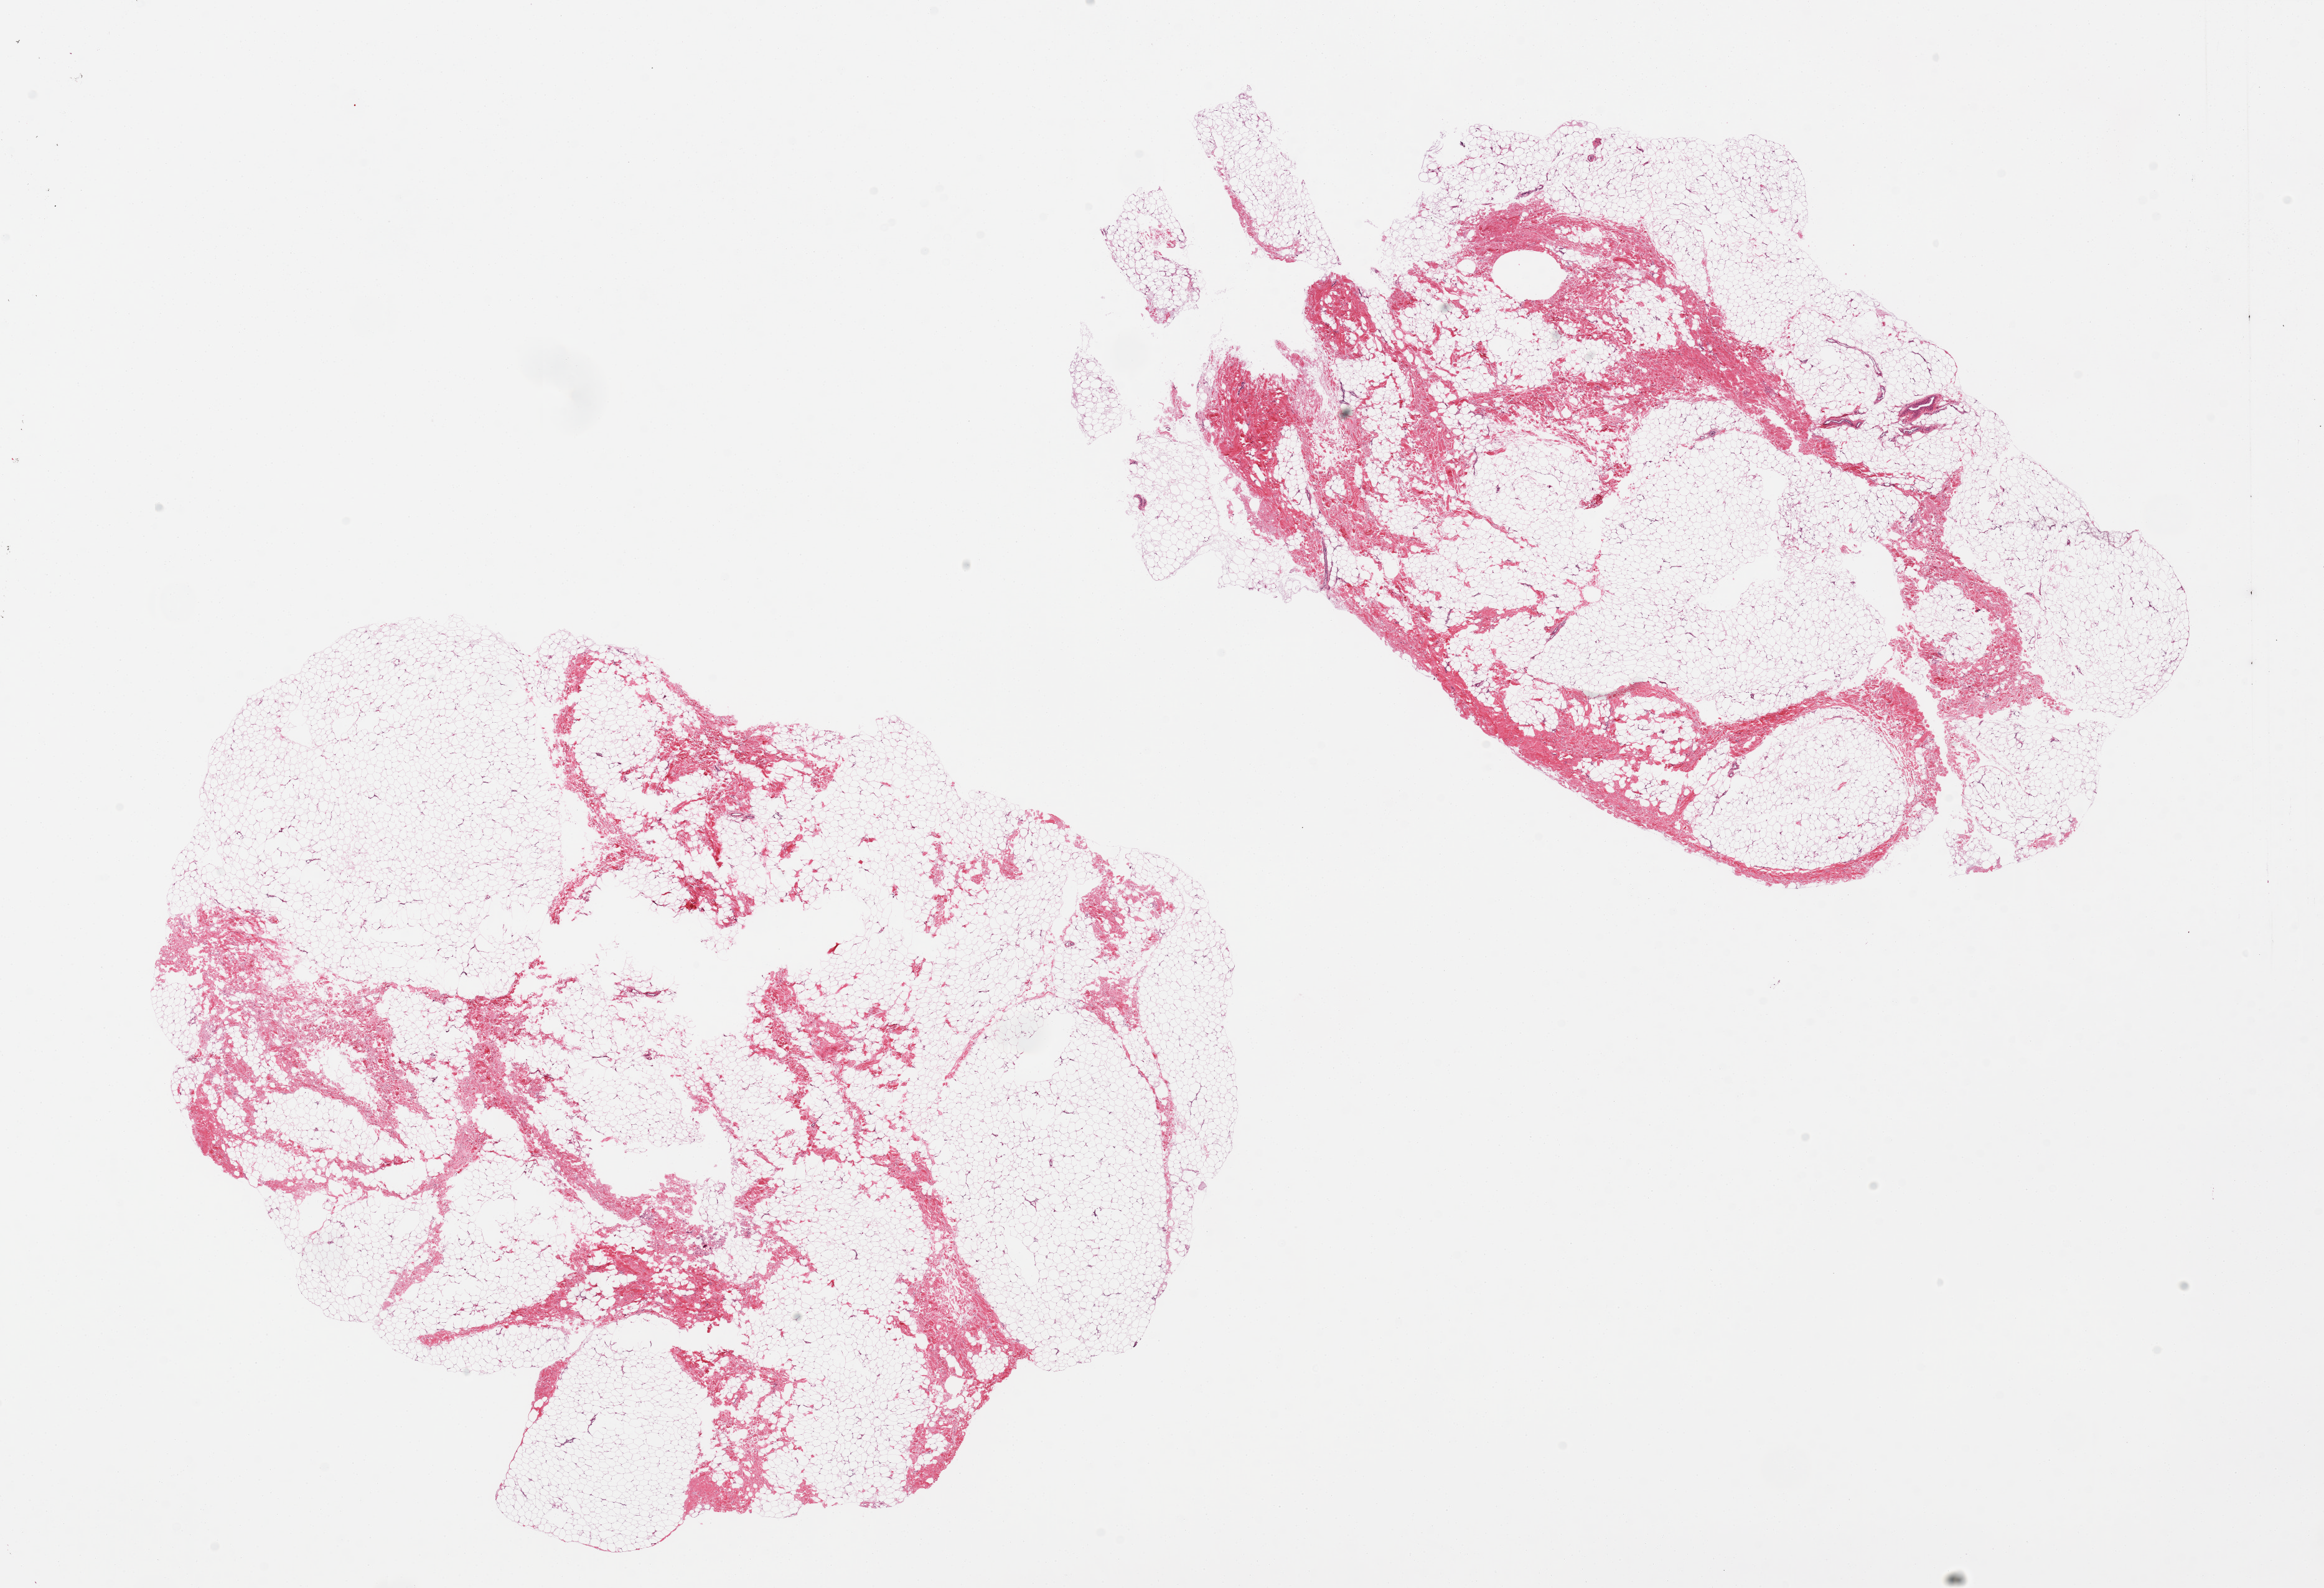
H&E whole-slide image, brightfield, whole scanned area (about 29.5 x 20.2 mm) shown as a low-resolution overview, PAXgene-fixed paraffin-embedded (PFPE) section, target tissue: breast, tissue donor sample. Donor: male.
Reviewer comment on this tissue sample: 2 pieces, predominantly fat with ~10% fibrous stroma, no epithelium identified.